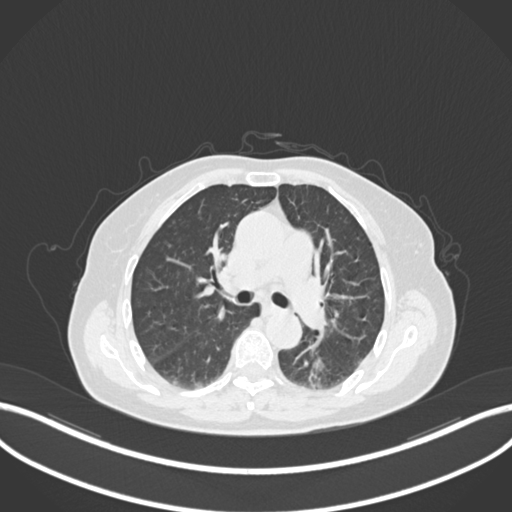
Chest CT, one axial slice. Position 528 of 727 along the scan axis. Reconstruction kernel B30f. Lung window (W 1500 / L -600 HU). 512 × 512 image matrix. Female patient, age 70 years. From the clinical record (not read from this slice): clinical TNM (as recorded): T1c N0 M0.
Structures marked on this image (bounding box drawn by a radiologist):
- lung tumour (recorded histology: adenocarcinoma): box from (x=301, y=351) to (x=328, y=387) px